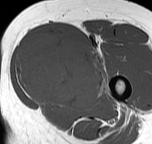
MRI of an extremity soft-tissue mass, one axial slice; position 29 of 57 along the scan axis; MR volume resampled by the dataset authors to the PET/CT grid (not the native acquisition matrix); 3.27 mm slice thickness; 152 × 144 image matrix, field of view 148 × 141 mm. Female patient. Case-level facts recorded for this patient, not image findings: histological type: pleiomorphic leiomyosarcoma; grade: intermediate; site of the primary tumour: left thigh.
Structures marked on this image (expert contour drawn on MRI and transferred to this co-registered scan by the dataset authors):
- gross tumour volume including surrounding oedema: bounding box <15,35,106,109> (left, top, right, bottom; pixels)
- gross tumour volume (mass): <15,35,103,107>